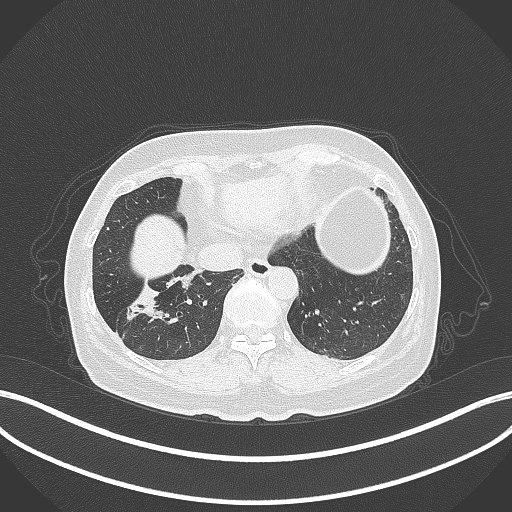
Chest CT, one axial slice; slice 103 of 429 in the series (ordered by position); reconstruction kernel B70f; lung window (W 1500 / L -600 HU); 512 × 512 image matrix, field of view 400 × 400 mm. Patient: female, 67 years. From the clinical record (not read from this slice): clinical TNM (as recorded): T1c N1 M0; histopathological grade: G2-3.
Outlined on this slice (bounding box drawn by a radiologist):
- lung tumour (recorded histology: adenocarcinoma): bounding box [x1, y1, x2, y2] px = [126, 275, 196, 332]